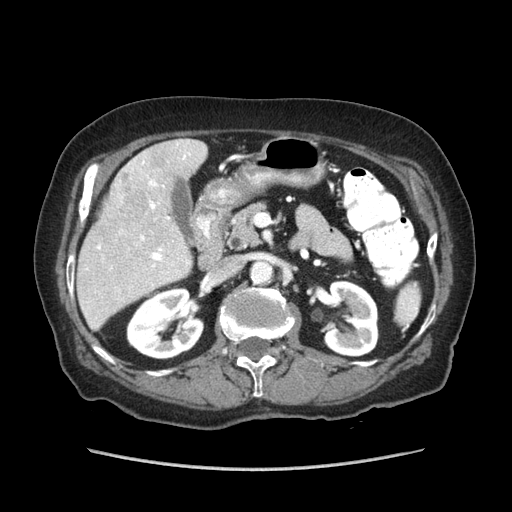
Contrast-enhanced abdominal CT (liver protocol), one axial slice. Position 33 of 89 along the scan axis. Reconstruction kernel STANDARD. 140 kVp. Soft-tissue window (W 400 / L 40 HU). 2.5 mm slice thickness. 512 × 512 image matrix. Case-level facts recorded for this patient, not image findings: diagnosis: hepatocellular carcinoma (patient treated with transarterial chemoembolisation; whether this scan precedes or follows treatment is not stated here); TNM stage (as recorded): Stage-IIIA; Child-Pugh class: A; tumour differentiation: well differentiated; tumour nodularity: multinodular.
Structures marked on this image (semi-automatically segmented with operator editing):
- liver parenchyma outside the tumour (the mass and vessels are separate outlines, so this box may not span the whole liver): bounding box (x1, y1, x2, y2) in pixels: (78, 138, 207, 330)
- mass: (105, 152, 161, 220)
- liver vessels: (97, 152, 191, 267)